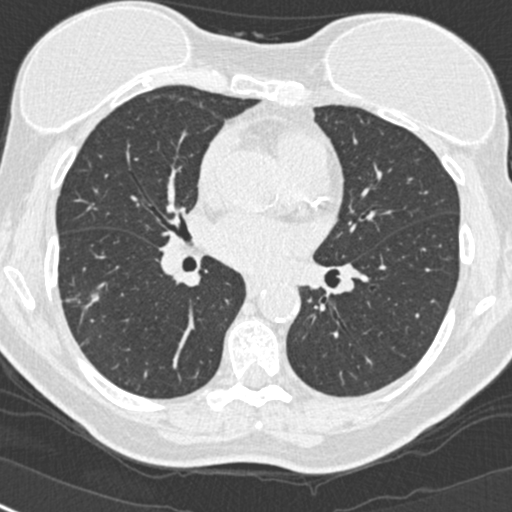
Low-dose screening chest CT, one axial slice; slice 134 of 268 in the series (ordered by position); reconstruction kernel B30f; lung window (W 1500 / L -600 HU); 512 × 512 image matrix, field of view 296 × 296 mm.
Outlined on this slice (outlined manually by an expert reader):
- lesion 1 (tumor, upper lobe of right lung): bounding box (x1, y1, x2, y2) in pixels: (82, 294, 99, 309)